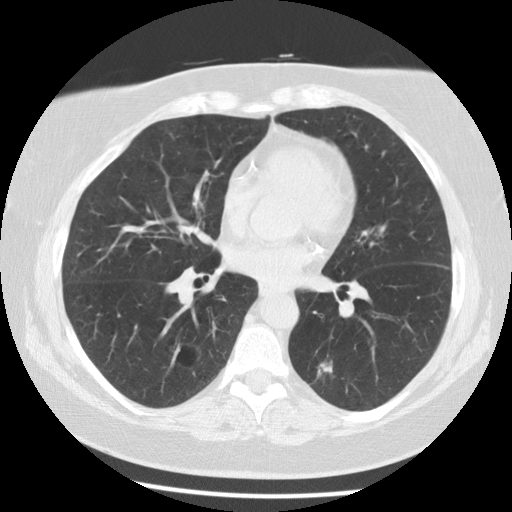
Axial slice from a low-dose chest CT screening exam; third screening round (two years after baseline); lung window (W 1500 / L -600 HU); 2.5 mm slice thickness; 512 × 512 image matrix. Female participant, aged 59 years at enrolment. Current smoker at enrolment.
- Expert reader's lesion annotation, box from (x=287, y=347) to (x=356, y=405) px.
- The screening reader recorded 6 non-calcified nodules or masses ≥4 mm on this exam (right lower lobe, right upper lobe, right lower lobe, right lower lobe, left lower lobe, left lower lobe); which of them this box marks is not recorded.
- Official screen result: positive, other.
- Participant outcome: lung cancer diagnosed 56 days after this screen — adenocarcinoma, NOS, left lower lobe, poorly differentiated (G3), stage IA (AJCC 6th edition), 15 mm at pathology.